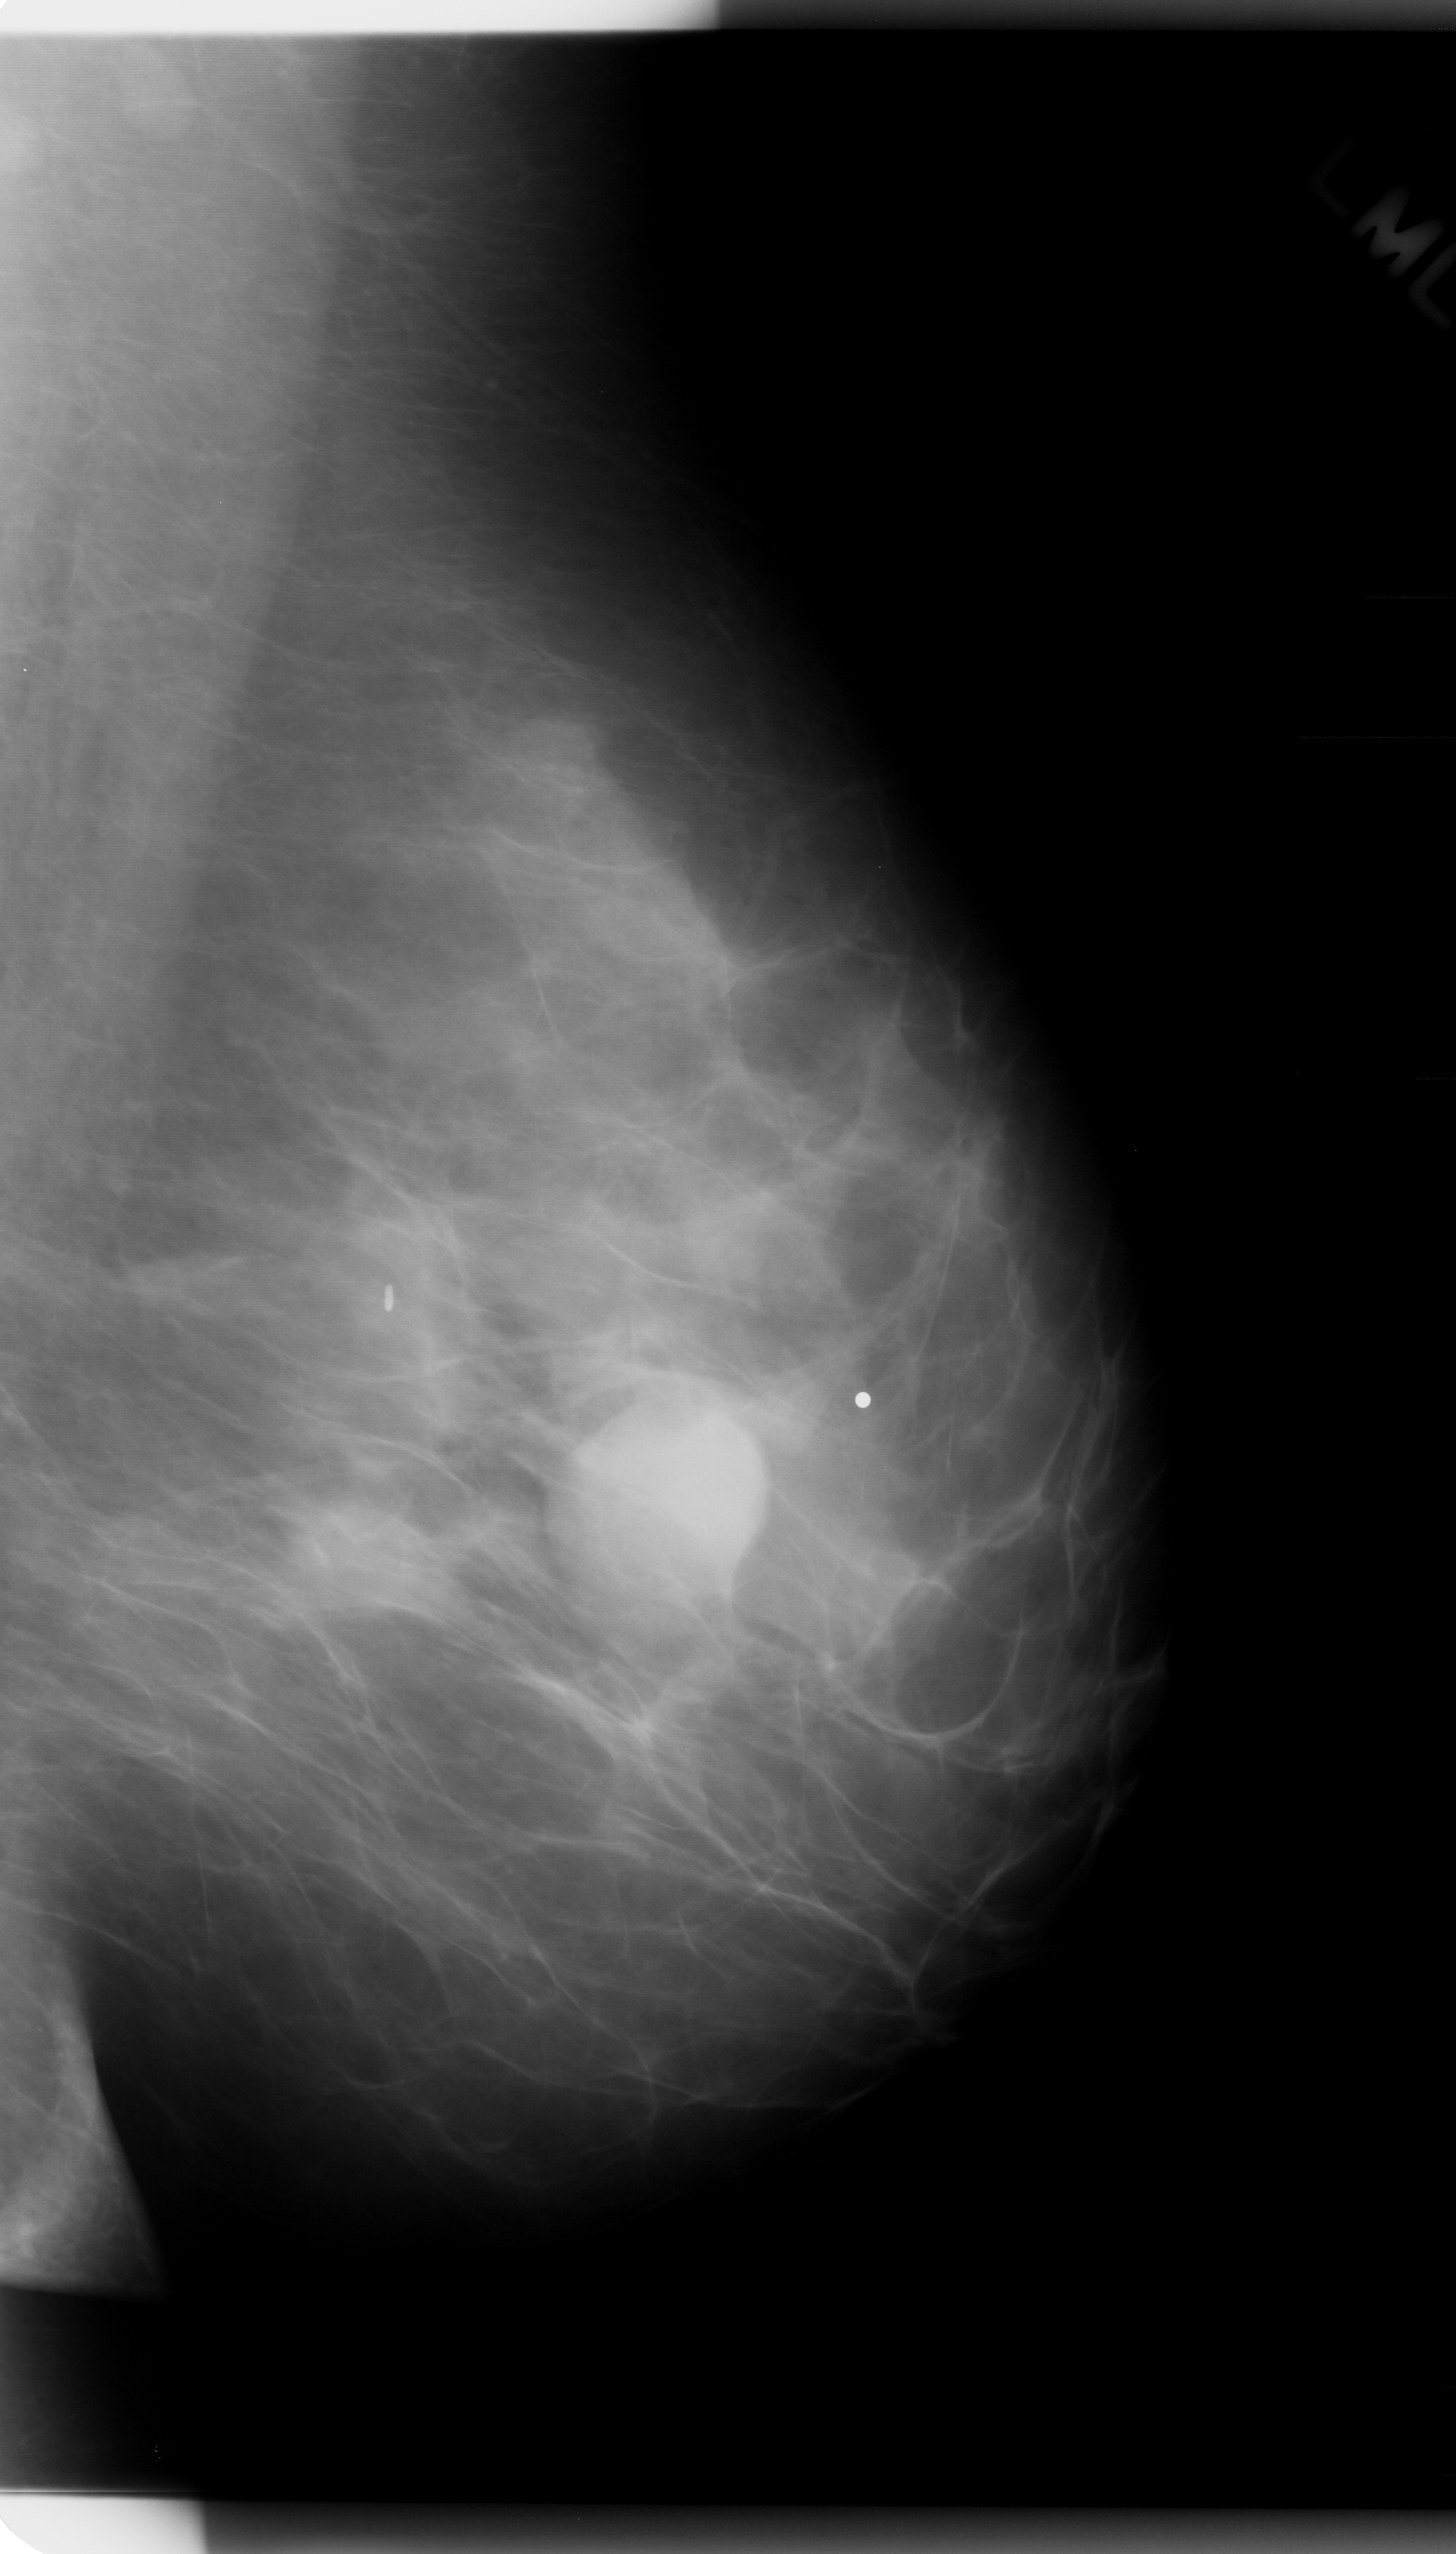
Digitized screen-film mammogram, left breast, mediolateral oblique (MLO) view, breast composition: scattered fibroglandular densities (BI-RADS density category 2 of 4).
- Marked abnormality: mass, shape round, margins obscured; BI-RADS assessment category 4; pathology (as recorded): benign.